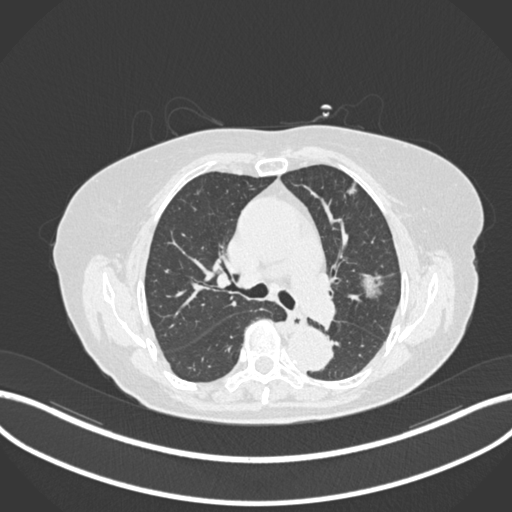
Chest CT, one axial slice; slice 100 of 168 in the series (ordered by position); 120 kVp; lung window (W 1500 / L -600 HU); 1 mm slice thickness; 512 × 512 image matrix, field of view 400 × 400 mm. Patient: female, 75 years. From the clinical record (not read from this slice): clinical TNM (as recorded): T1c N0 M0.
Annotated regions visible in this slice (bounding box drawn by a radiologist):
- lung tumour (recorded histology: adenocarcinoma): bounding box [x1, y1, x2, y2] px = [360, 268, 384, 301]